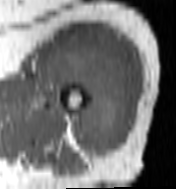
MRI of an extremity soft-tissue mass, one axial slice; slice 75 of 100 in the series (ordered by position); MR volume resampled by the dataset authors to the PET/CT grid (not the native acquisition matrix); 176 × 189 image matrix. Female patient. Case-level facts recorded for this patient, not image findings: histological type: undifferentiated – high grade; grade: high; site of the primary tumour: left thigh.
Annotated regions visible in this slice (expert contour drawn on MRI and transferred to this co-registered scan by the dataset authors):
- gross tumour volume including surrounding oedema: bounding box (x1, y1, x2, y2) in pixels: (44, 39, 132, 158)
- gross tumour volume (mass): (46, 39, 131, 158)